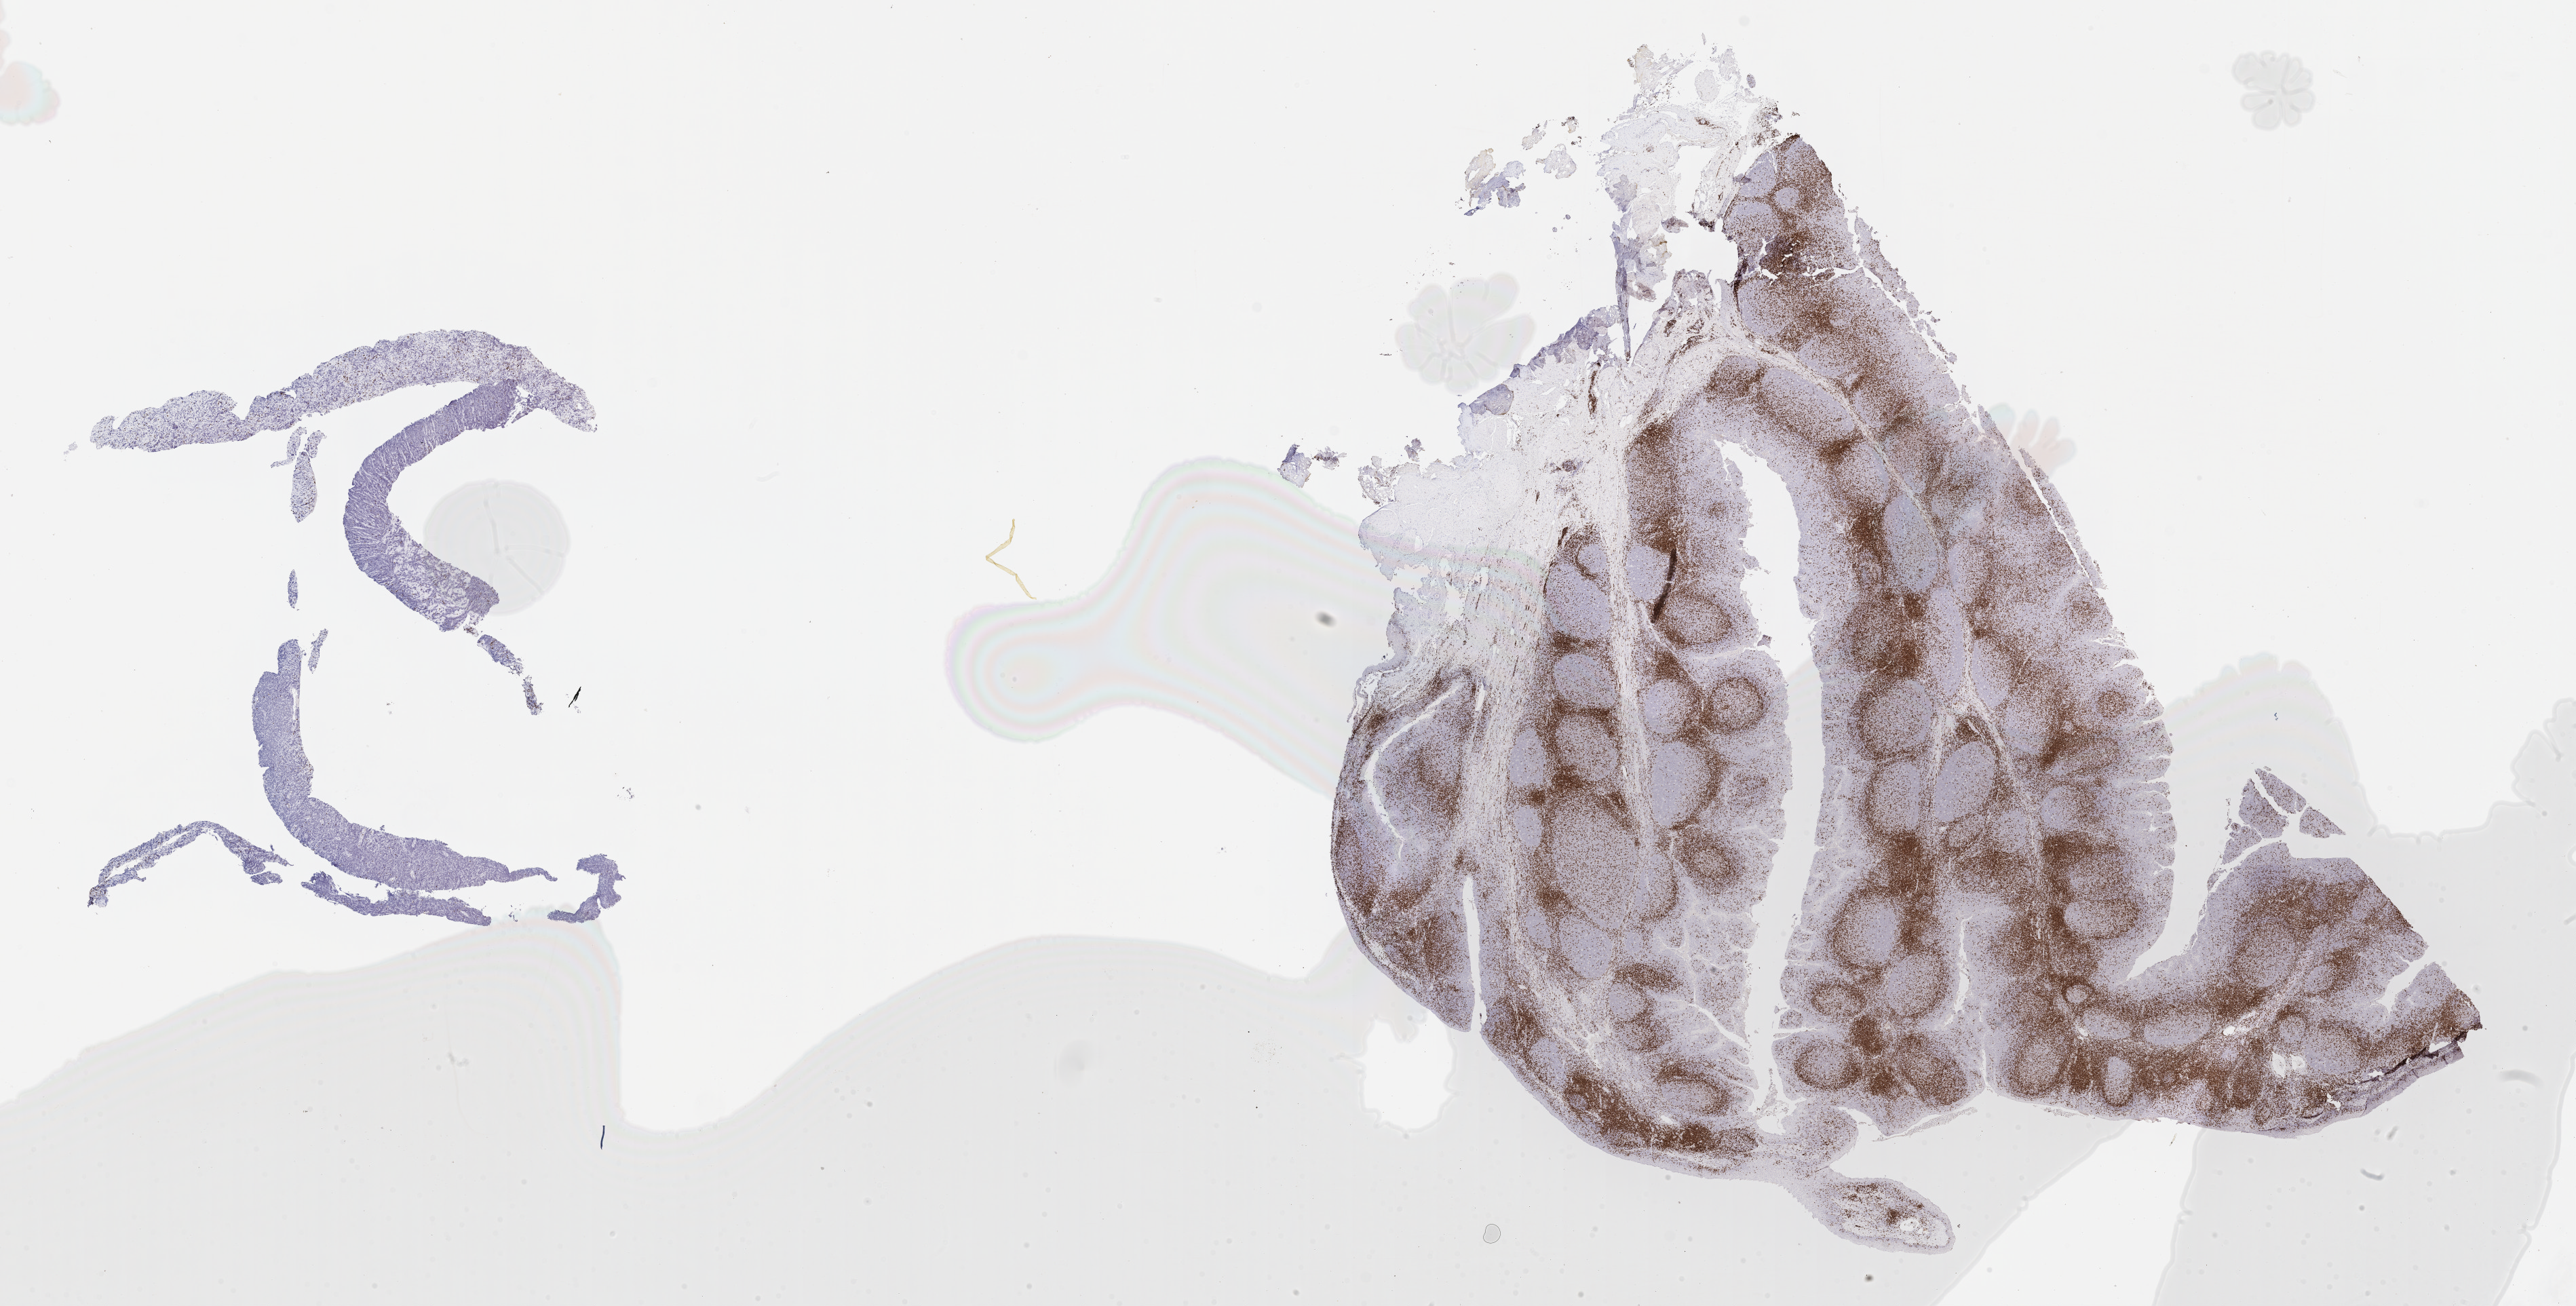
Immunohistochemistry (IHC) whole-slide image stained for CD3 — a low-resolution overview of the entire scanned area, about 30.7 x 15.6 mm, tumor tissue, site: pleura. Patient: male, age at initial diagnosis 2 years.
• diagnosis: Diffuse large B-cell lymphoma, NOS